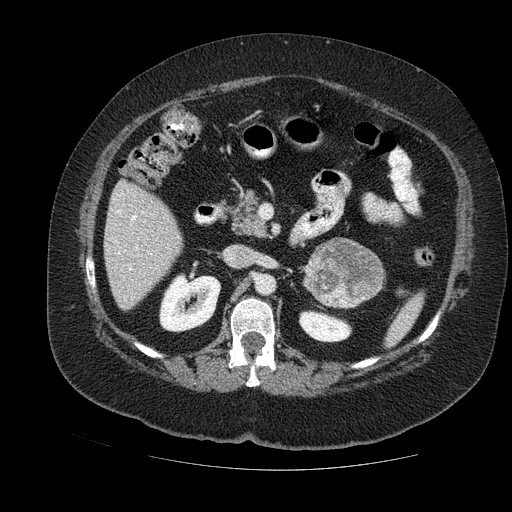
Contrast-enhanced abdominal CT, one axial slice; slice 64 of 121 in the series (ordered by position); soft-tissue window (W 400 / L 40 HU); 2.5 mm slice thickness; 512 × 512 image matrix, field of view 420 × 420 mm. Female patient. Case-level facts recorded for this patient, not image findings: diagnosis: adrenocortical carcinoma; tumour side: left adrenal; tumour size at pathology: 8 cm; Ki-67 index: 7 %; stage (as recorded): 2.
Outlined on this slice (semi-automatic segmentation, software-assisted and operator-edited):
- mass: bounding box (x1, y1, x2, y2) in pixels: (307, 240, 379, 306)